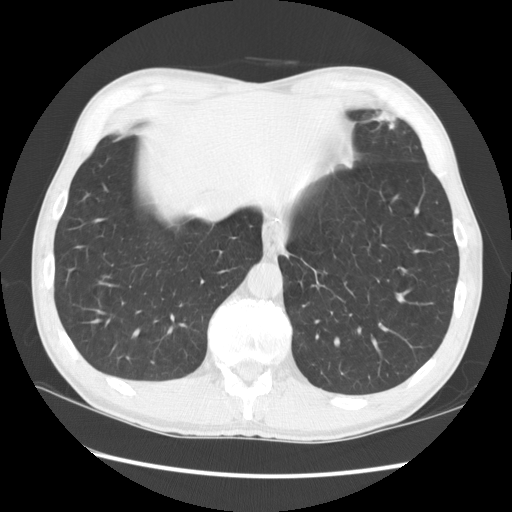
Low-dose screening chest CT, one axial slice; position 29 of 141 along the scan axis; reconstruction kernel STANDARD; lung window (W 1500 / L -600 HU); 2.5 mm slice thickness; 512 × 512 image matrix.
Outlined on this slice (expert manual segmentation):
- lesion 1 (tumor, lower lobe of left lung): box from (x=373, y=112) to (x=396, y=129) px